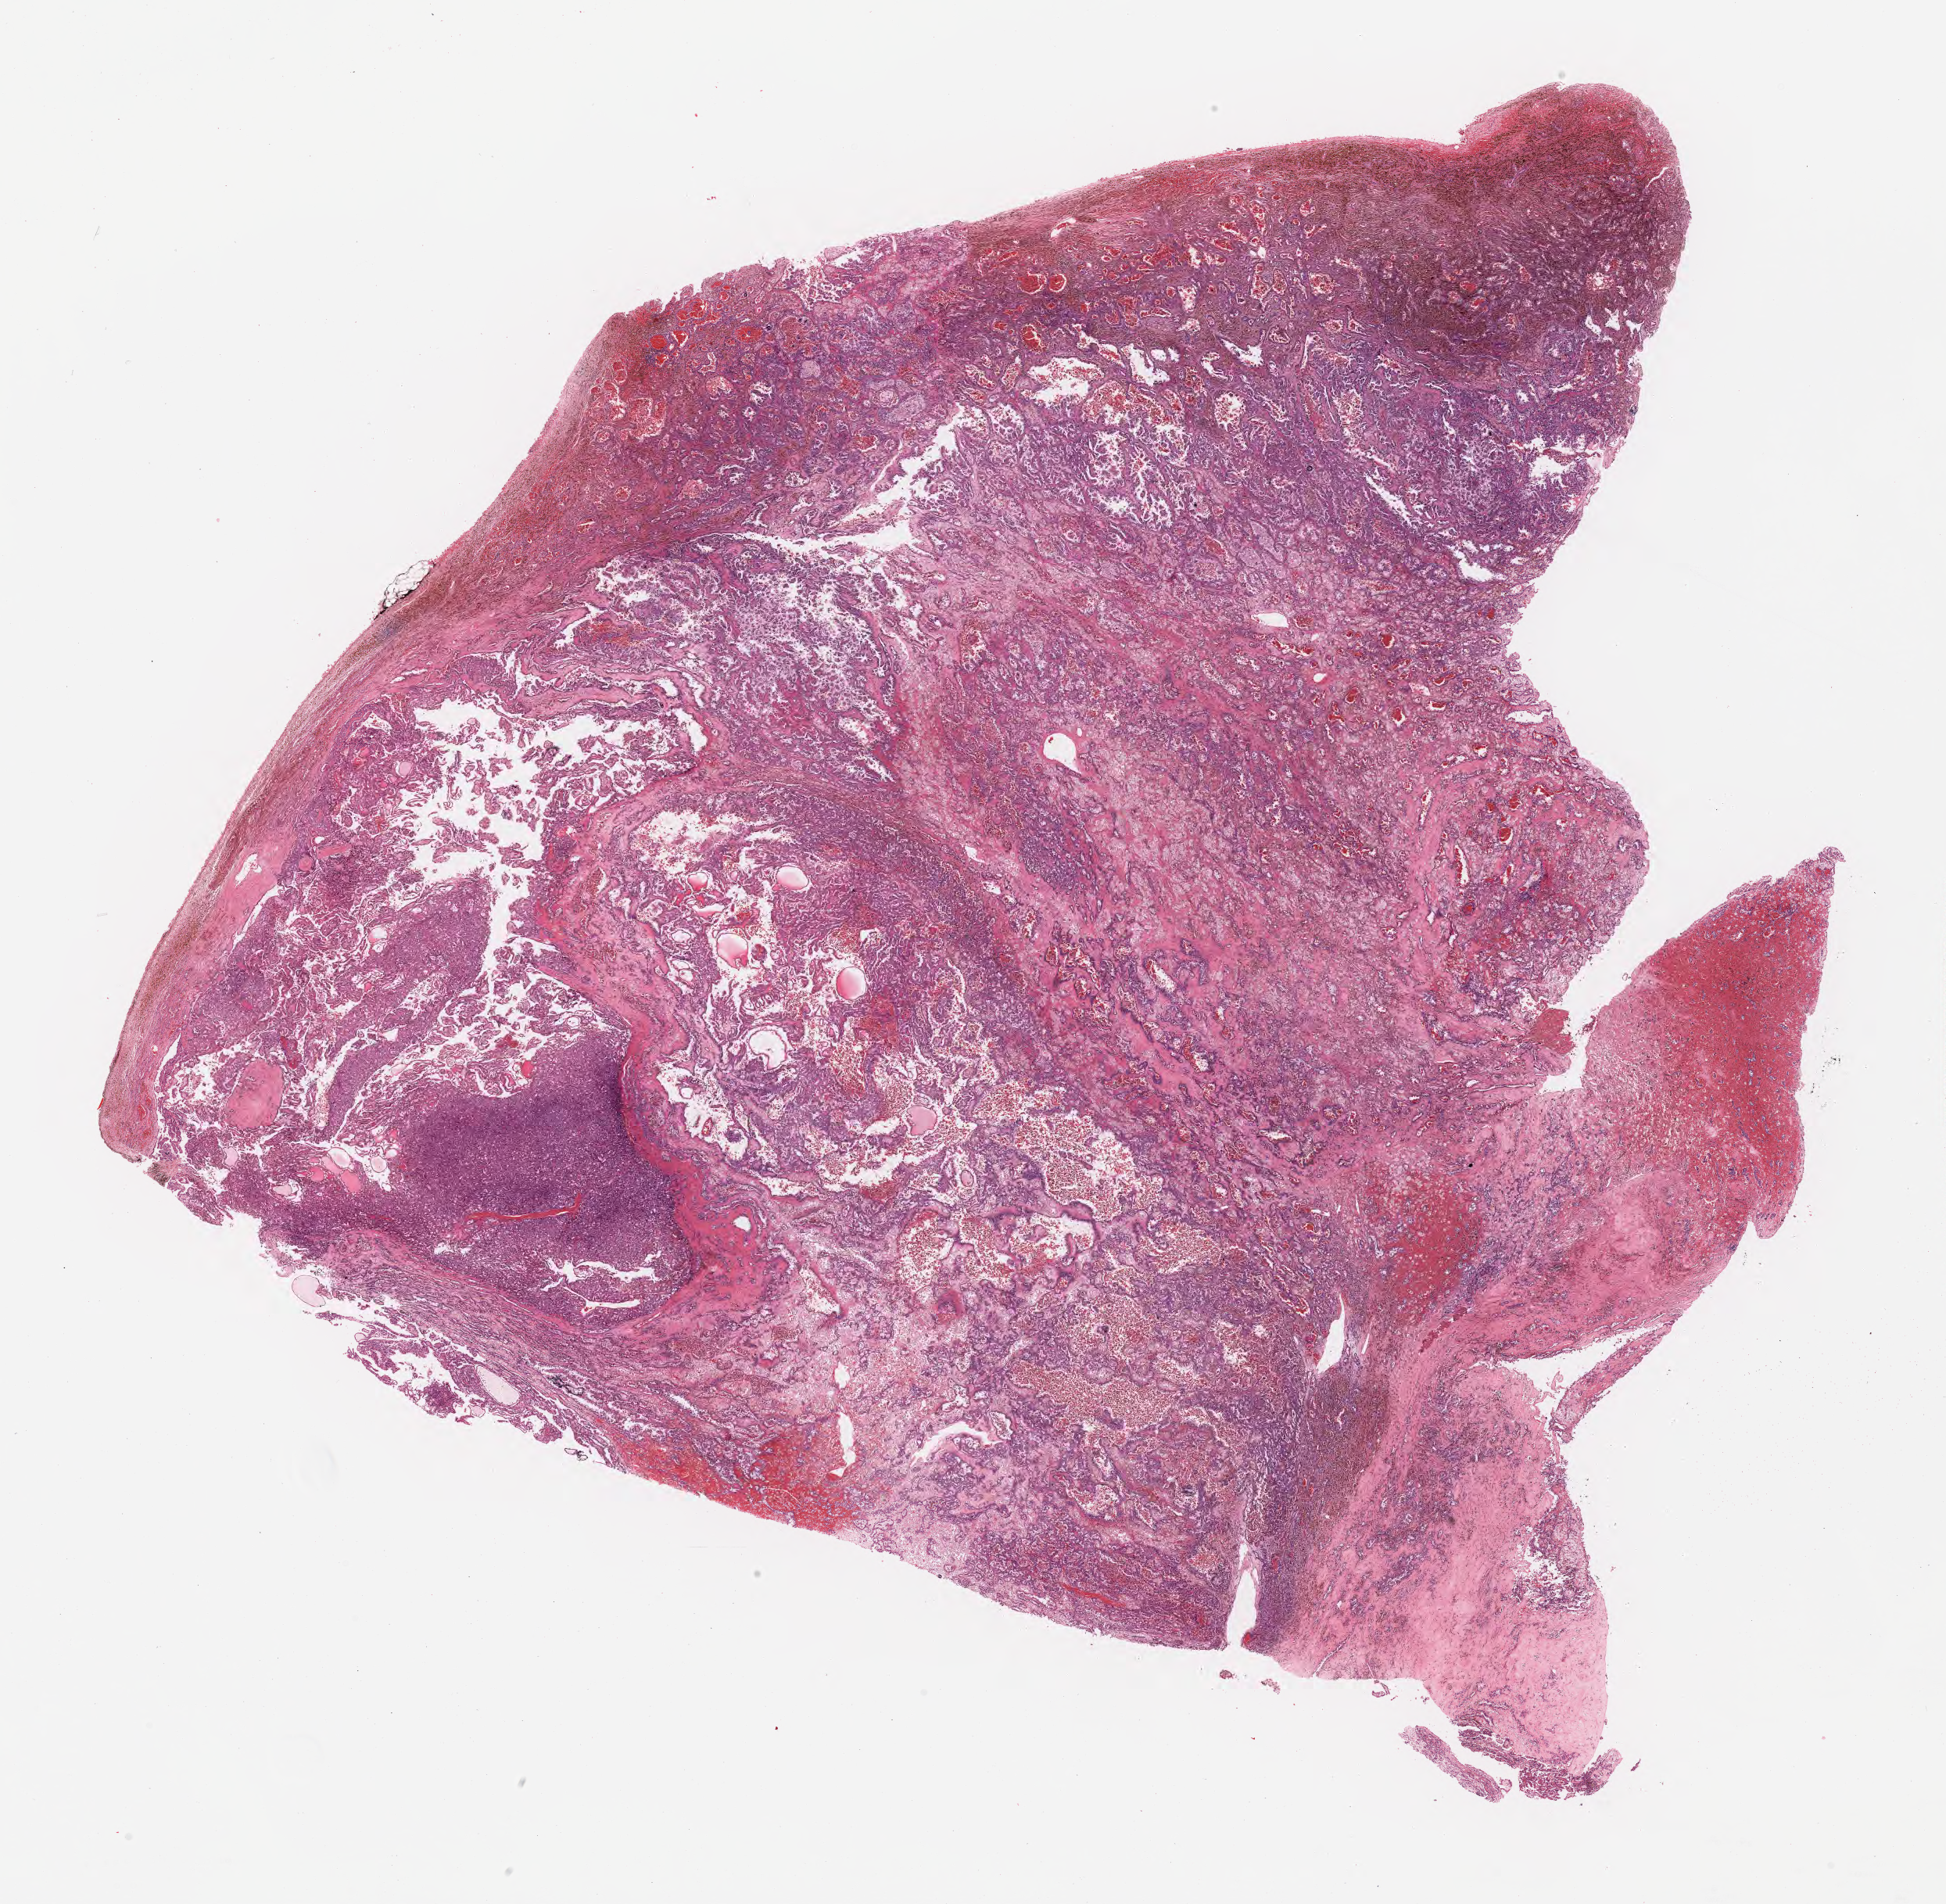
H&E whole-slide image — shown as a low-resolution overview of the whole scanned area (about 19.7 x 19.2 mm). Formalin-fixed paraffin-embedded (FFPE) diagnostic section. Kidney, primary tumour sample. Male, age 80 years at initial diagnosis.
* diagnosis: Papillary adenocarcinoma, NOS
* laterality: left